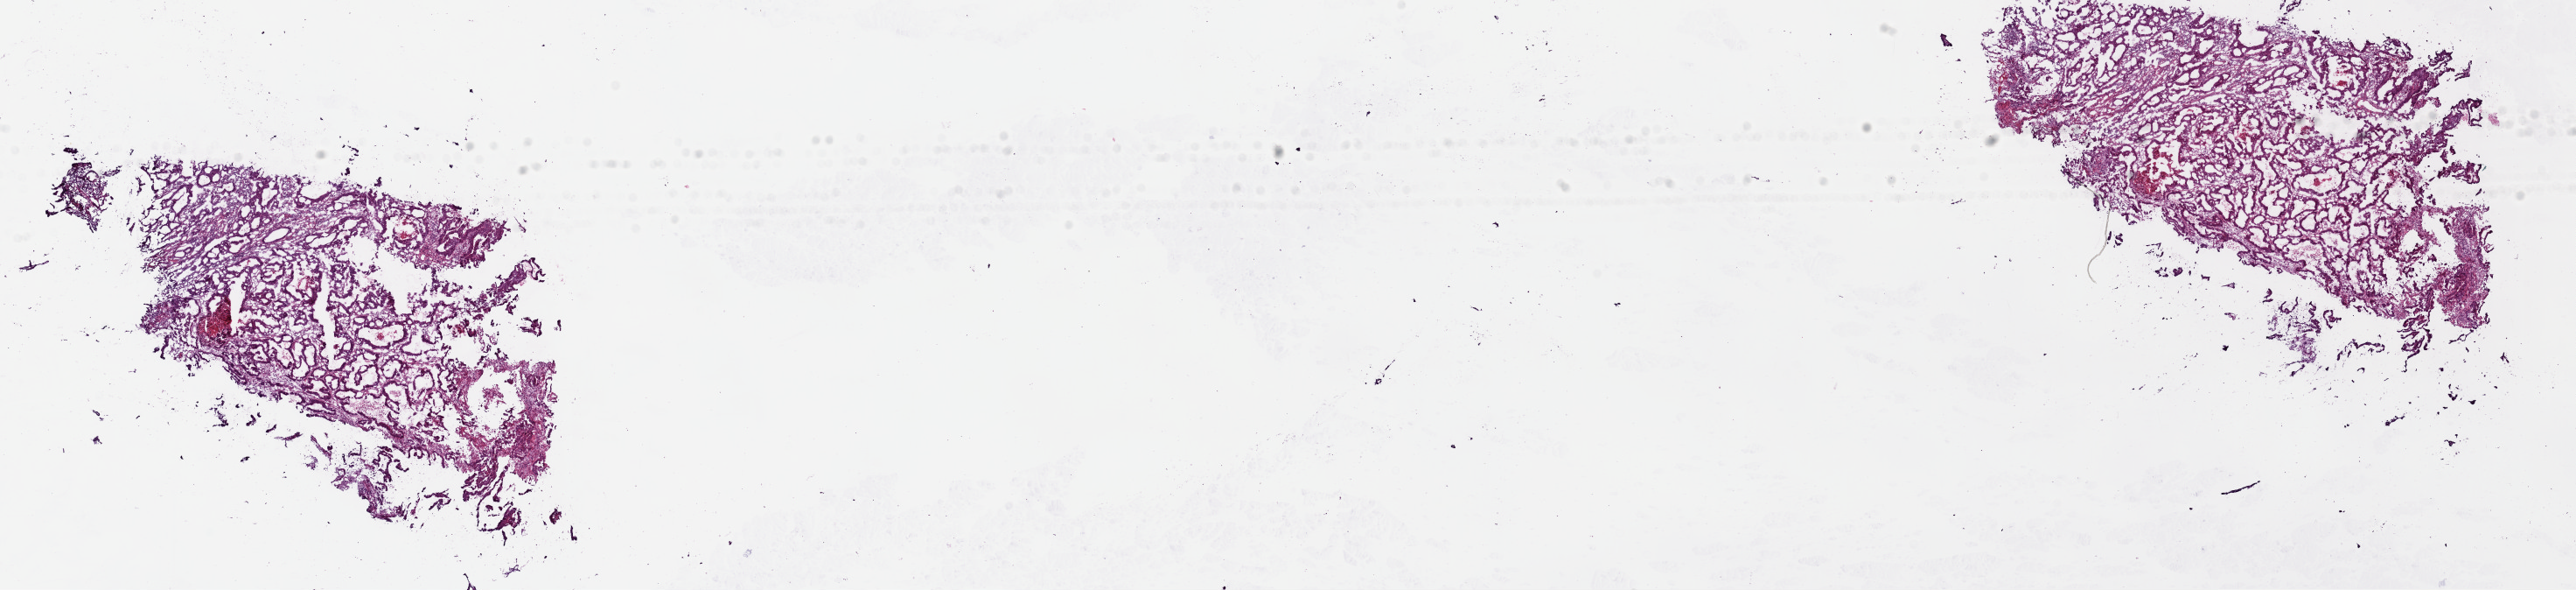
H&E whole-slide image — shown as a low-resolution overview of the whole scanned area (about 23.3 x 5.3 mm, acquisition: 40x scan), frozen section from the top of the tissue portion, primary tumour sample from the colon. Patient: male, age at initial diagnosis 73 years. Composition of this section per pathologist review: tumour cells 80%, tumour nuclei 80%, normal cells 0%, stromal cells 17%, necrosis 3%. Inflammatory infiltration, as recorded: lymphocyte infiltration 2%, monocyte infiltration 1%, neutrophil infiltration 1%.
Lymph nodes positive (case pathology): 1 of 23 examined. TNM: T3 N1 M0. AJCC pathologic stage: IIIB (6th edition). Diagnosis: Adenocarcinoma, NOS.